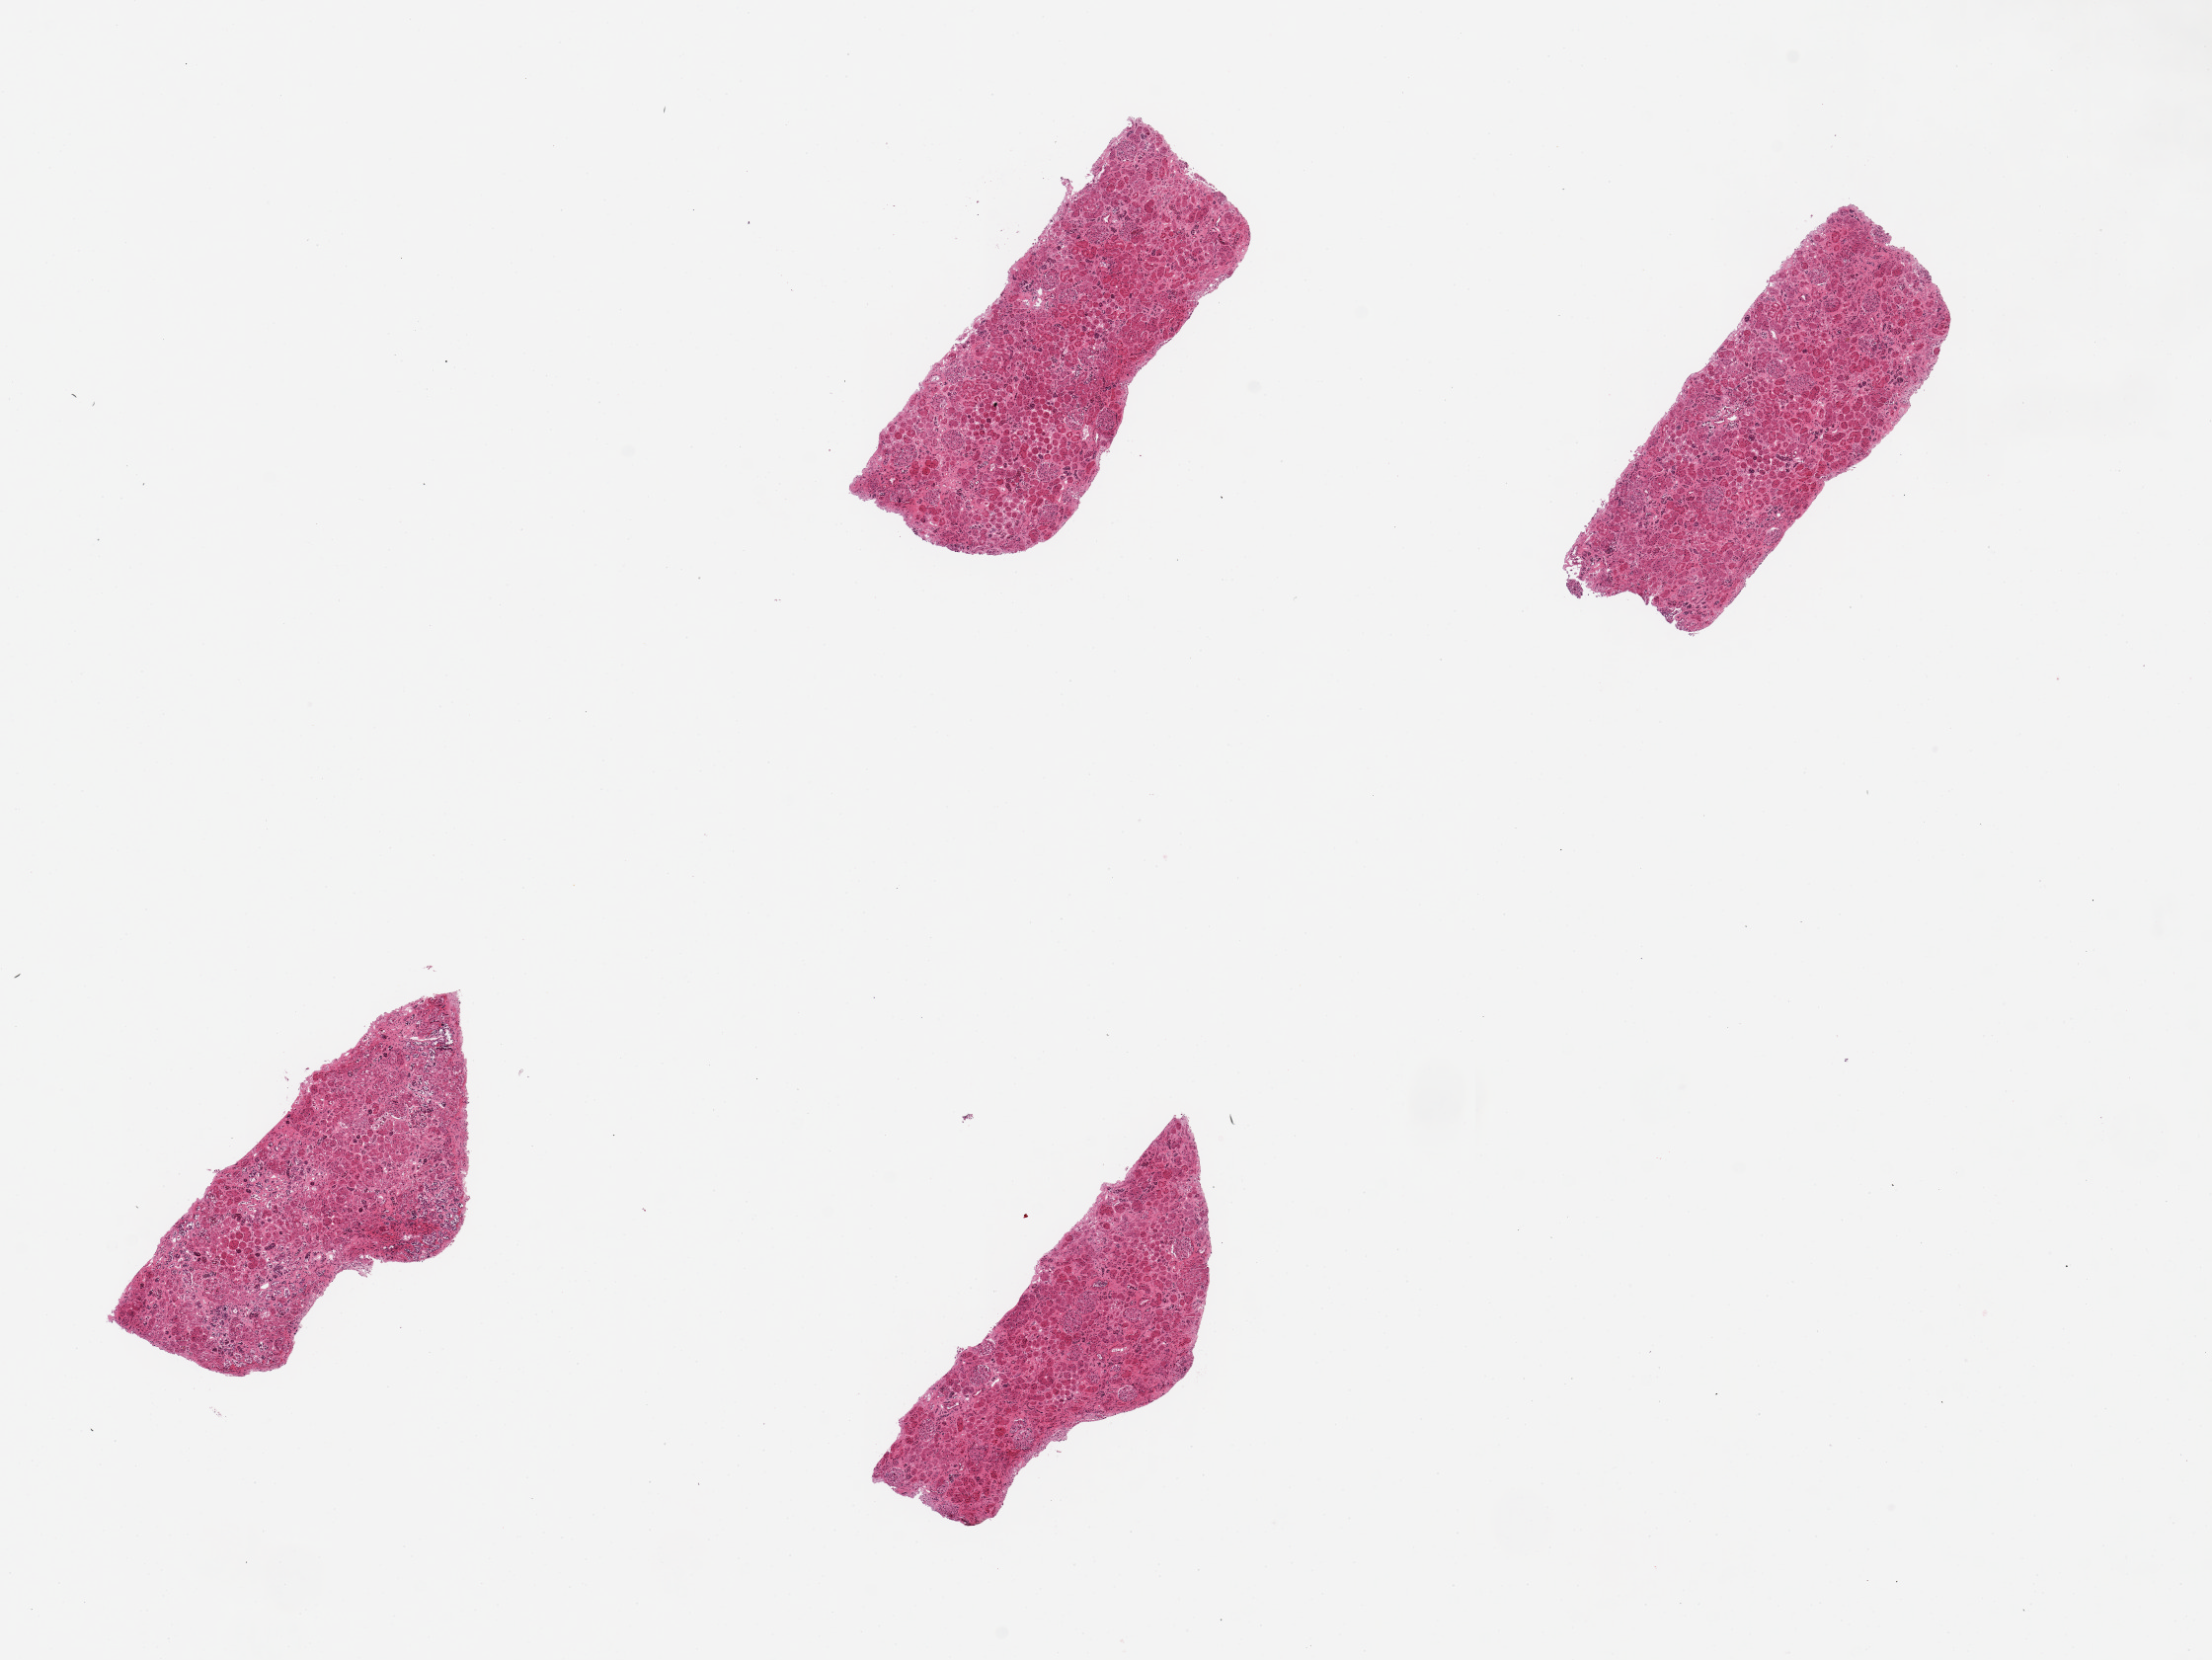
Digitized hematoxylin and eosin (H&E)-stained section — whole scanned area (about 17.7 x 13.3 mm, acquisition: 20x scan) shown as a low-resolution overview; PAXgene-fixed paraffin-embedded (PFPE) section; target tissue: renal cortex; donor tissue sample. Donor sex: male.
Reviewer comment on this tissue sample: 4 pieces, up to 4x2mm.